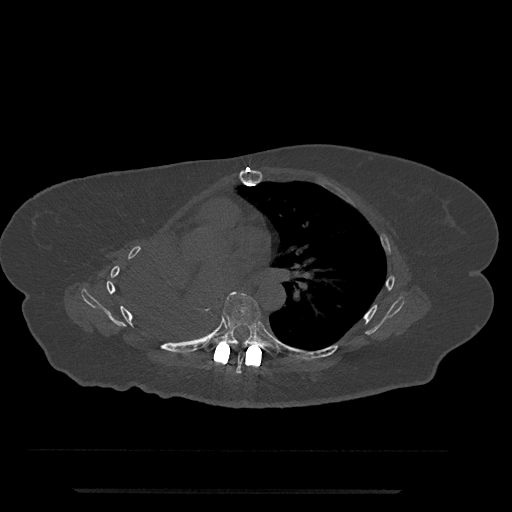
CT including the spine, one axial slice; 120 kVp; bone window (W 1800 / L 400 HU); 0.5 mm slice thickness; 512 × 512 image matrix. Female patient, age 51 years. From the clinical record (not read from this slice): primary cancer: neuro.
Structures marked on this image (semi-automatic segmentation, software-assisted and operator-edited):
- T6 vertebra: bounding box <236,354,244,373> (left, top, right, bottom; pixels)
- T7 vertebra: <204,292,279,357>